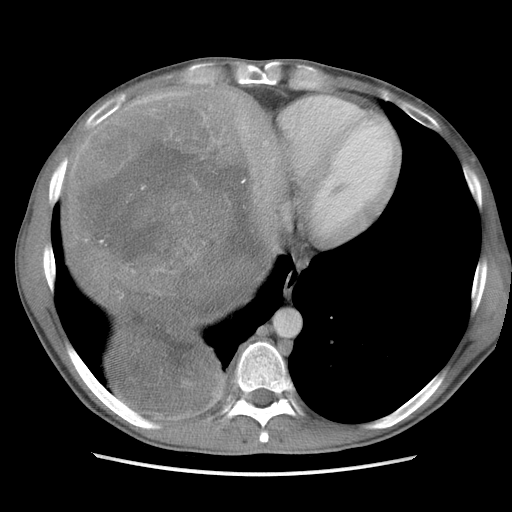
Contrast-enhanced abdominal CT, one axial slice. Slice 93 of 115 in the series (ordered by position). Soft-tissue window (W 400 / L 40 HU). 512 × 512 image matrix, field of view 360 × 360 mm. Male patient. Case-level facts recorded for this patient, not image findings: diagnosis: adrenocortical carcinoma; tumour side: right adrenal; Ki-67 index: 13 %; stage (as recorded): 3.
Annotated regions visible in this slice (semi-automatic segmentation, software-assisted and operator-edited):
- mass: box from (x=72, y=90) to (x=280, y=416) px